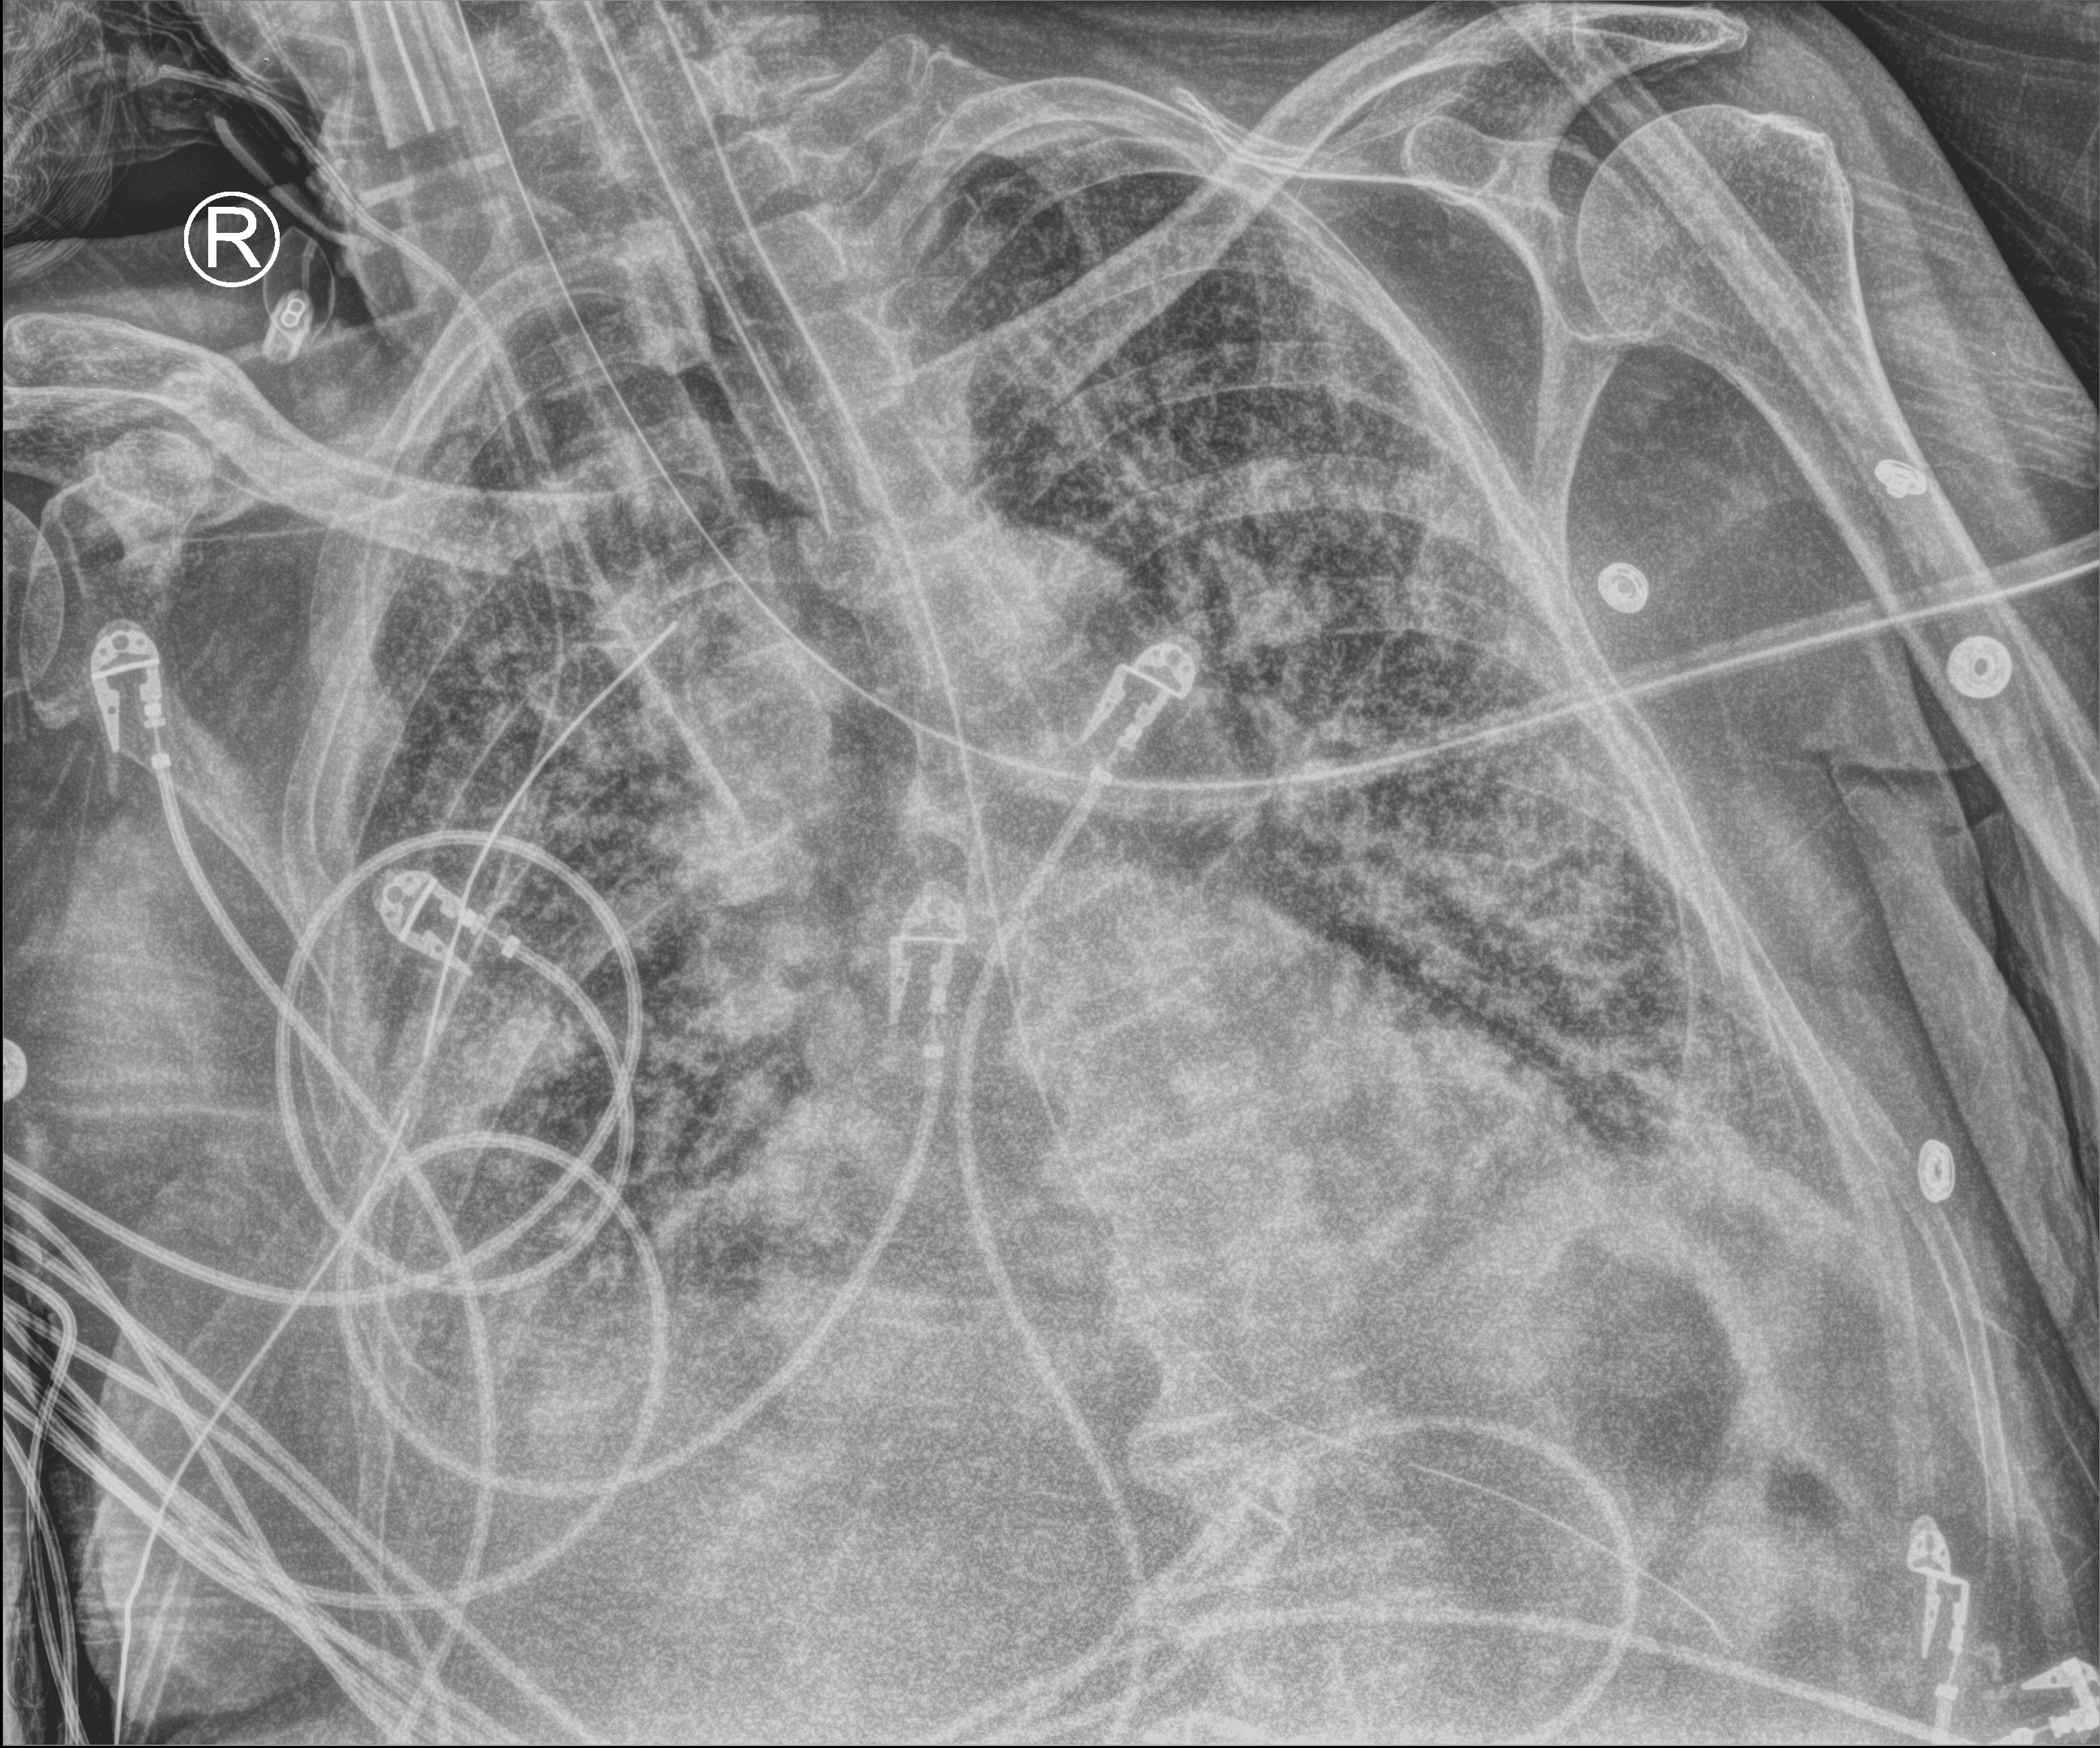
Chest X-ray (portable); anteroposterior (AP) projection. Patient hospitalised with COVID-19; male, aged 75–90 years.
Admission-level facts for this patient (not findings on this image; timing relative to this image not recorded):
- mechanically ventilated during this hospital stay: yes
- admitted to intensive care during this hospital stay: yes